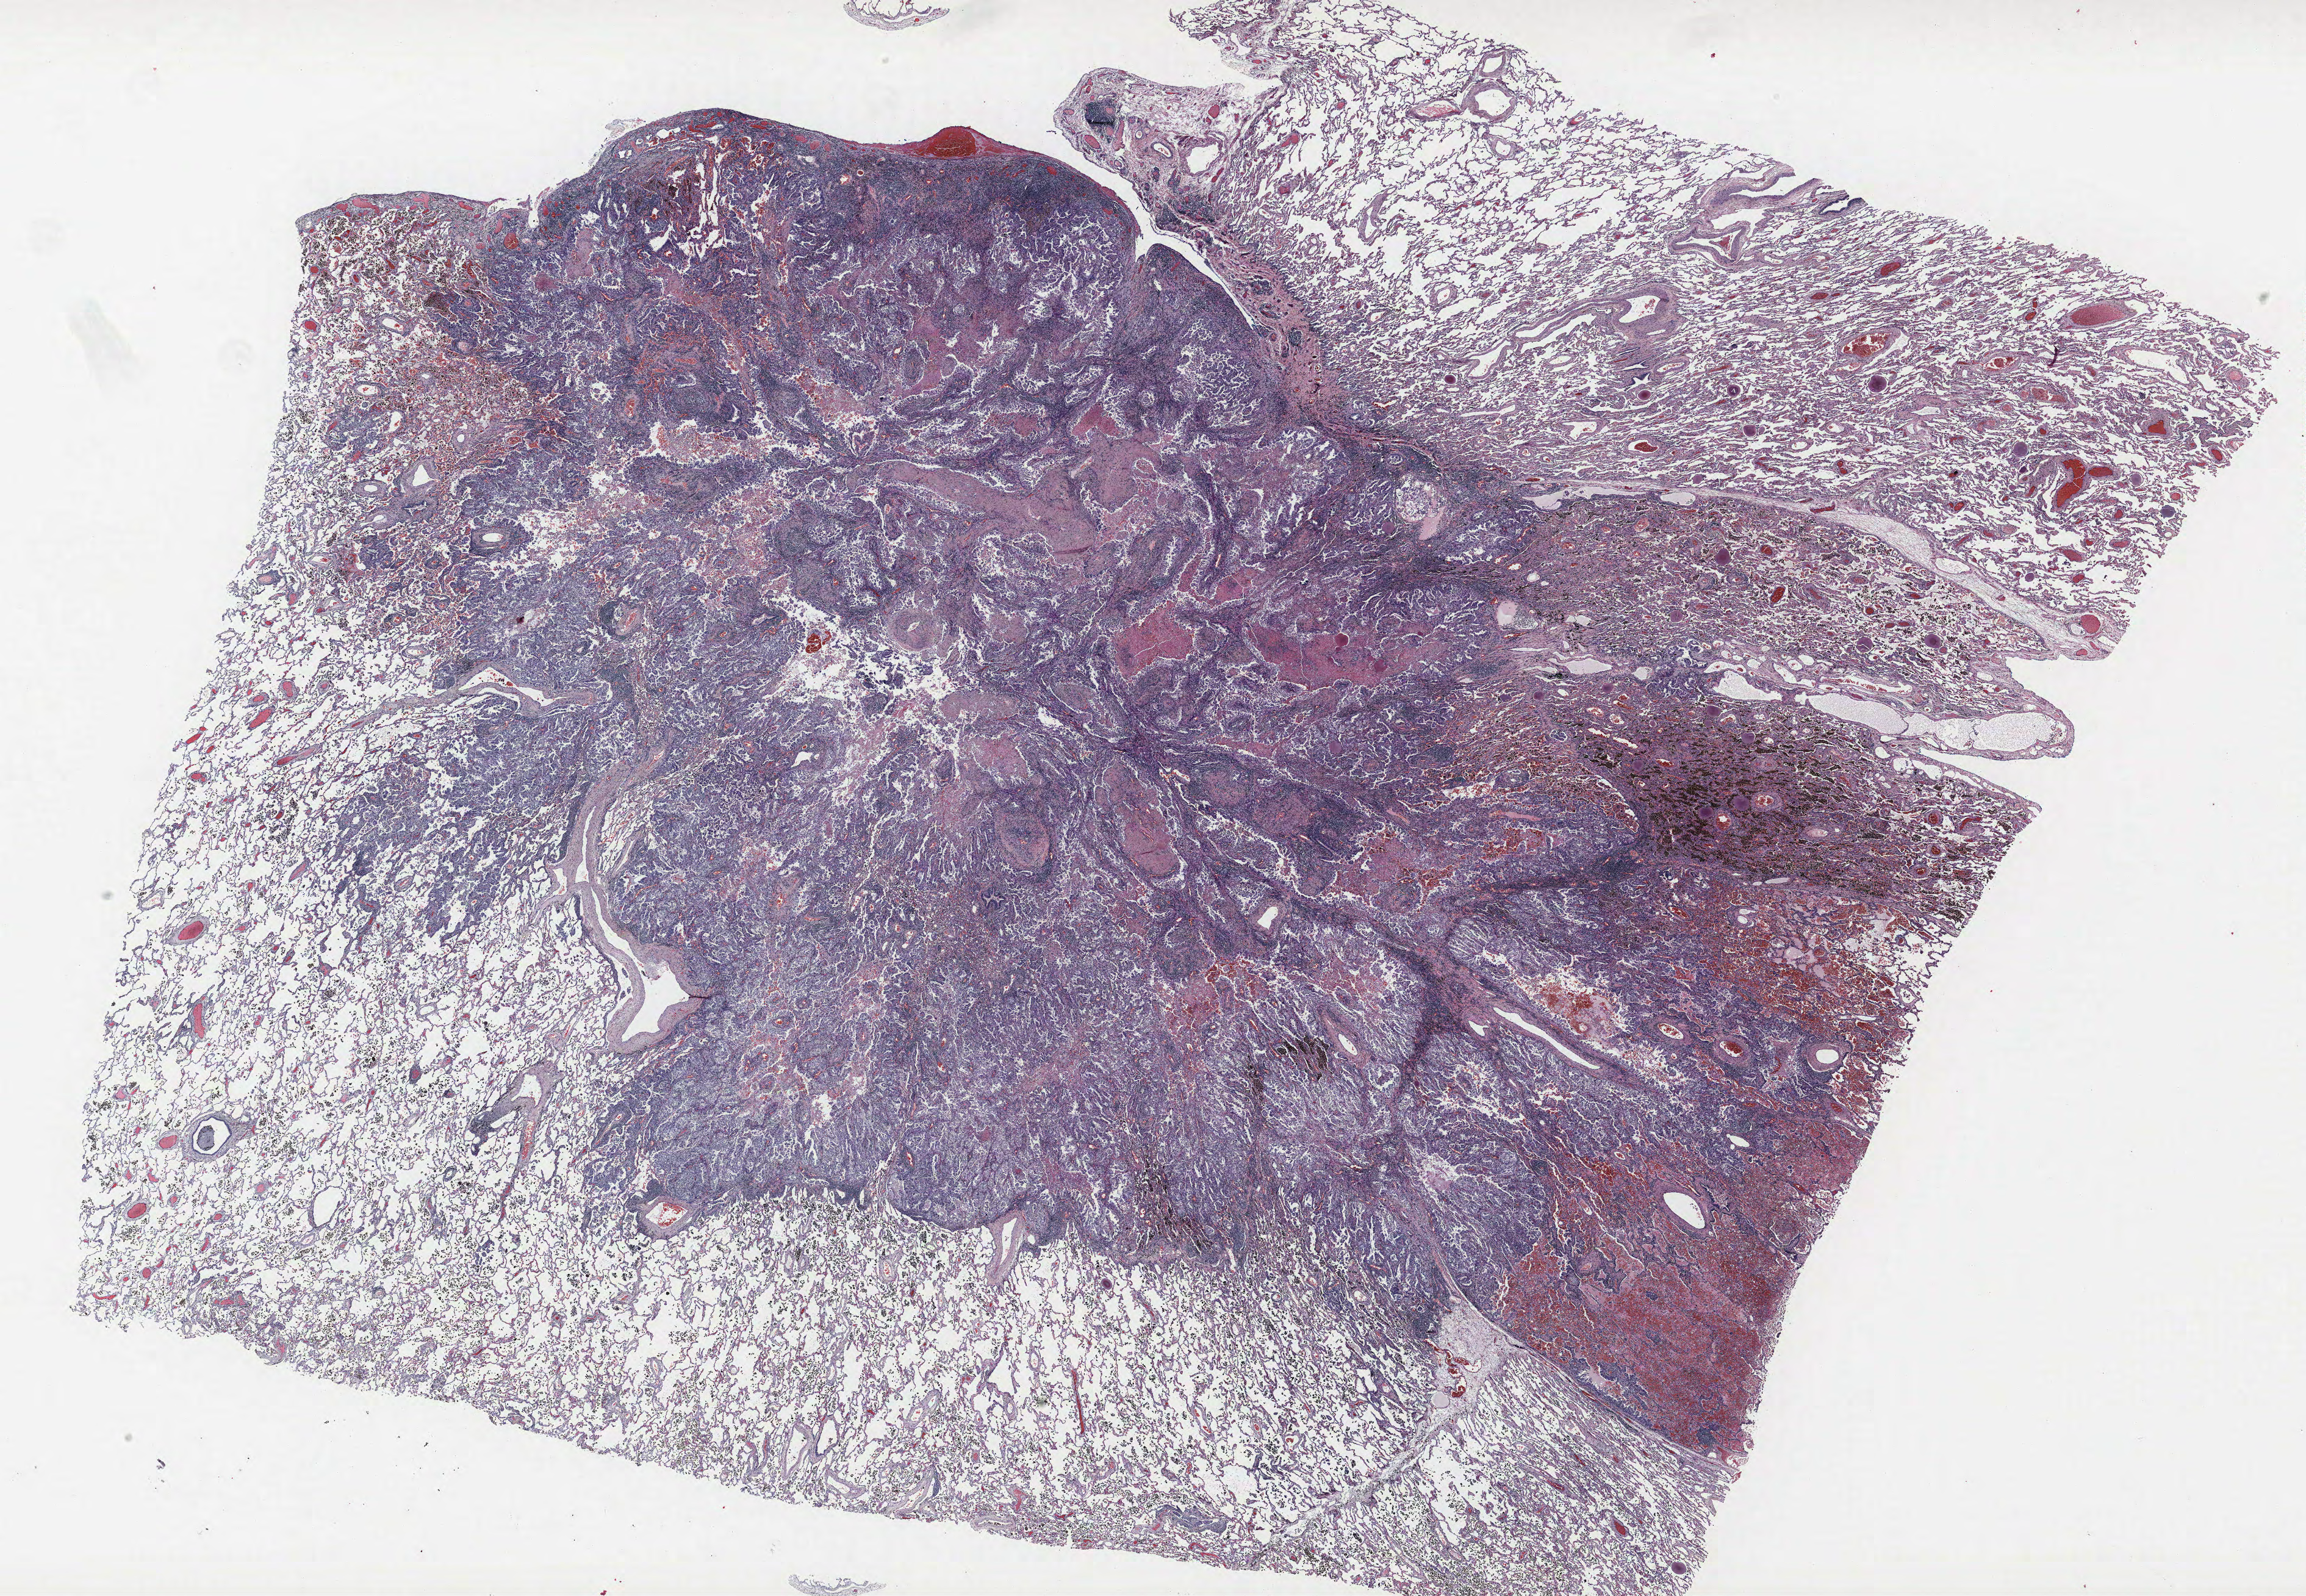
Whole-slide histology image, Hematoxylin and eosin (H&E) stained, shown as a low-resolution overview of the whole scanned area (about 30.2 x 20.9 mm), formalin-fixed paraffin-embedded (FFPE) section, lung tissue. Female, age 60 at enrolment.
Participant's lung-cancer diagnosis: Adenocarcinoma, NOS.